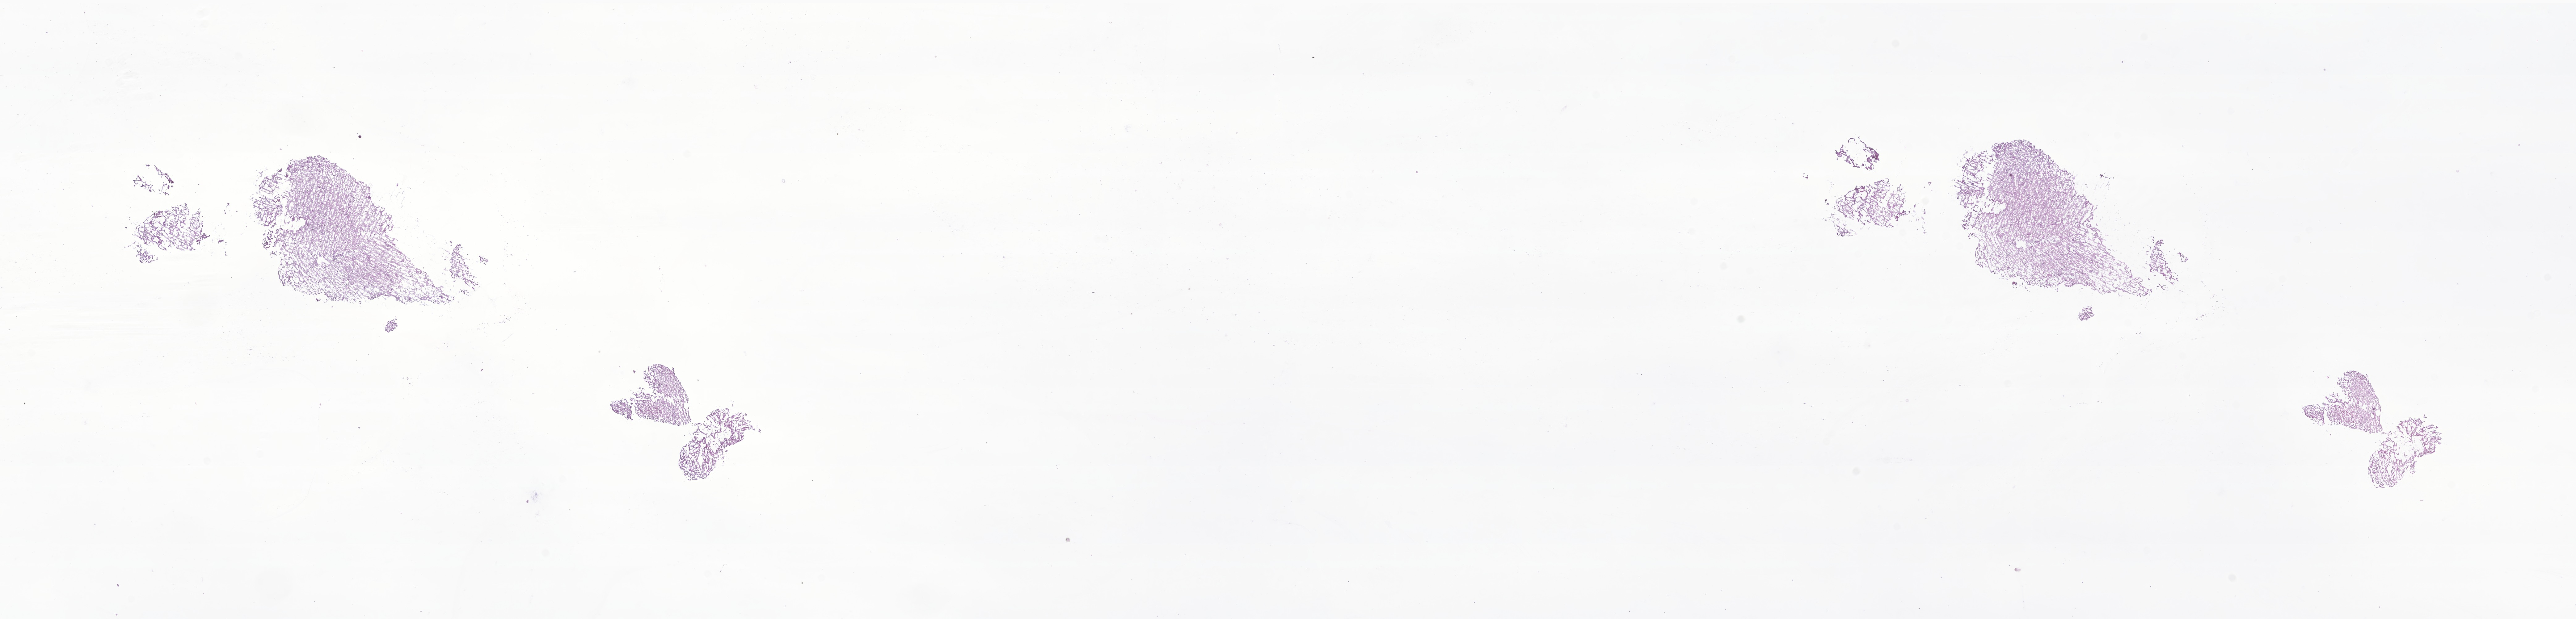
Digitized H&E-stained section of tumor tissue from the temporal lobe — low-resolution overview of the scanned area, about 35.2 x 8.5 mm; frozen section. Male patient, age 129 months (10 years 9 months).
Diagnosis (ICD-O-3 morphology term): Pilocytic astrocytoma.